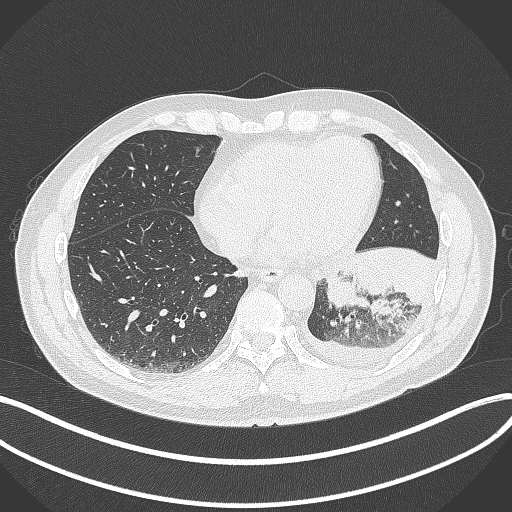
Chest CT, one axial slice. Slice 113 of 342 in the series (ordered by position). 120 kVp. Lung window (W 1500 / L -600 HU). 1 mm slice thickness. 512 × 512 image matrix. Patient: male, 58 years. From the clinical record (not read from this slice): clinical TNM (as recorded): T3 N1 M1b.
Outlined on this slice (bounding box drawn by a radiologist):
- lung tumour (recorded histology: small cell carcinoma): bounding box [x1, y1, x2, y2] px = [328, 267, 371, 311]